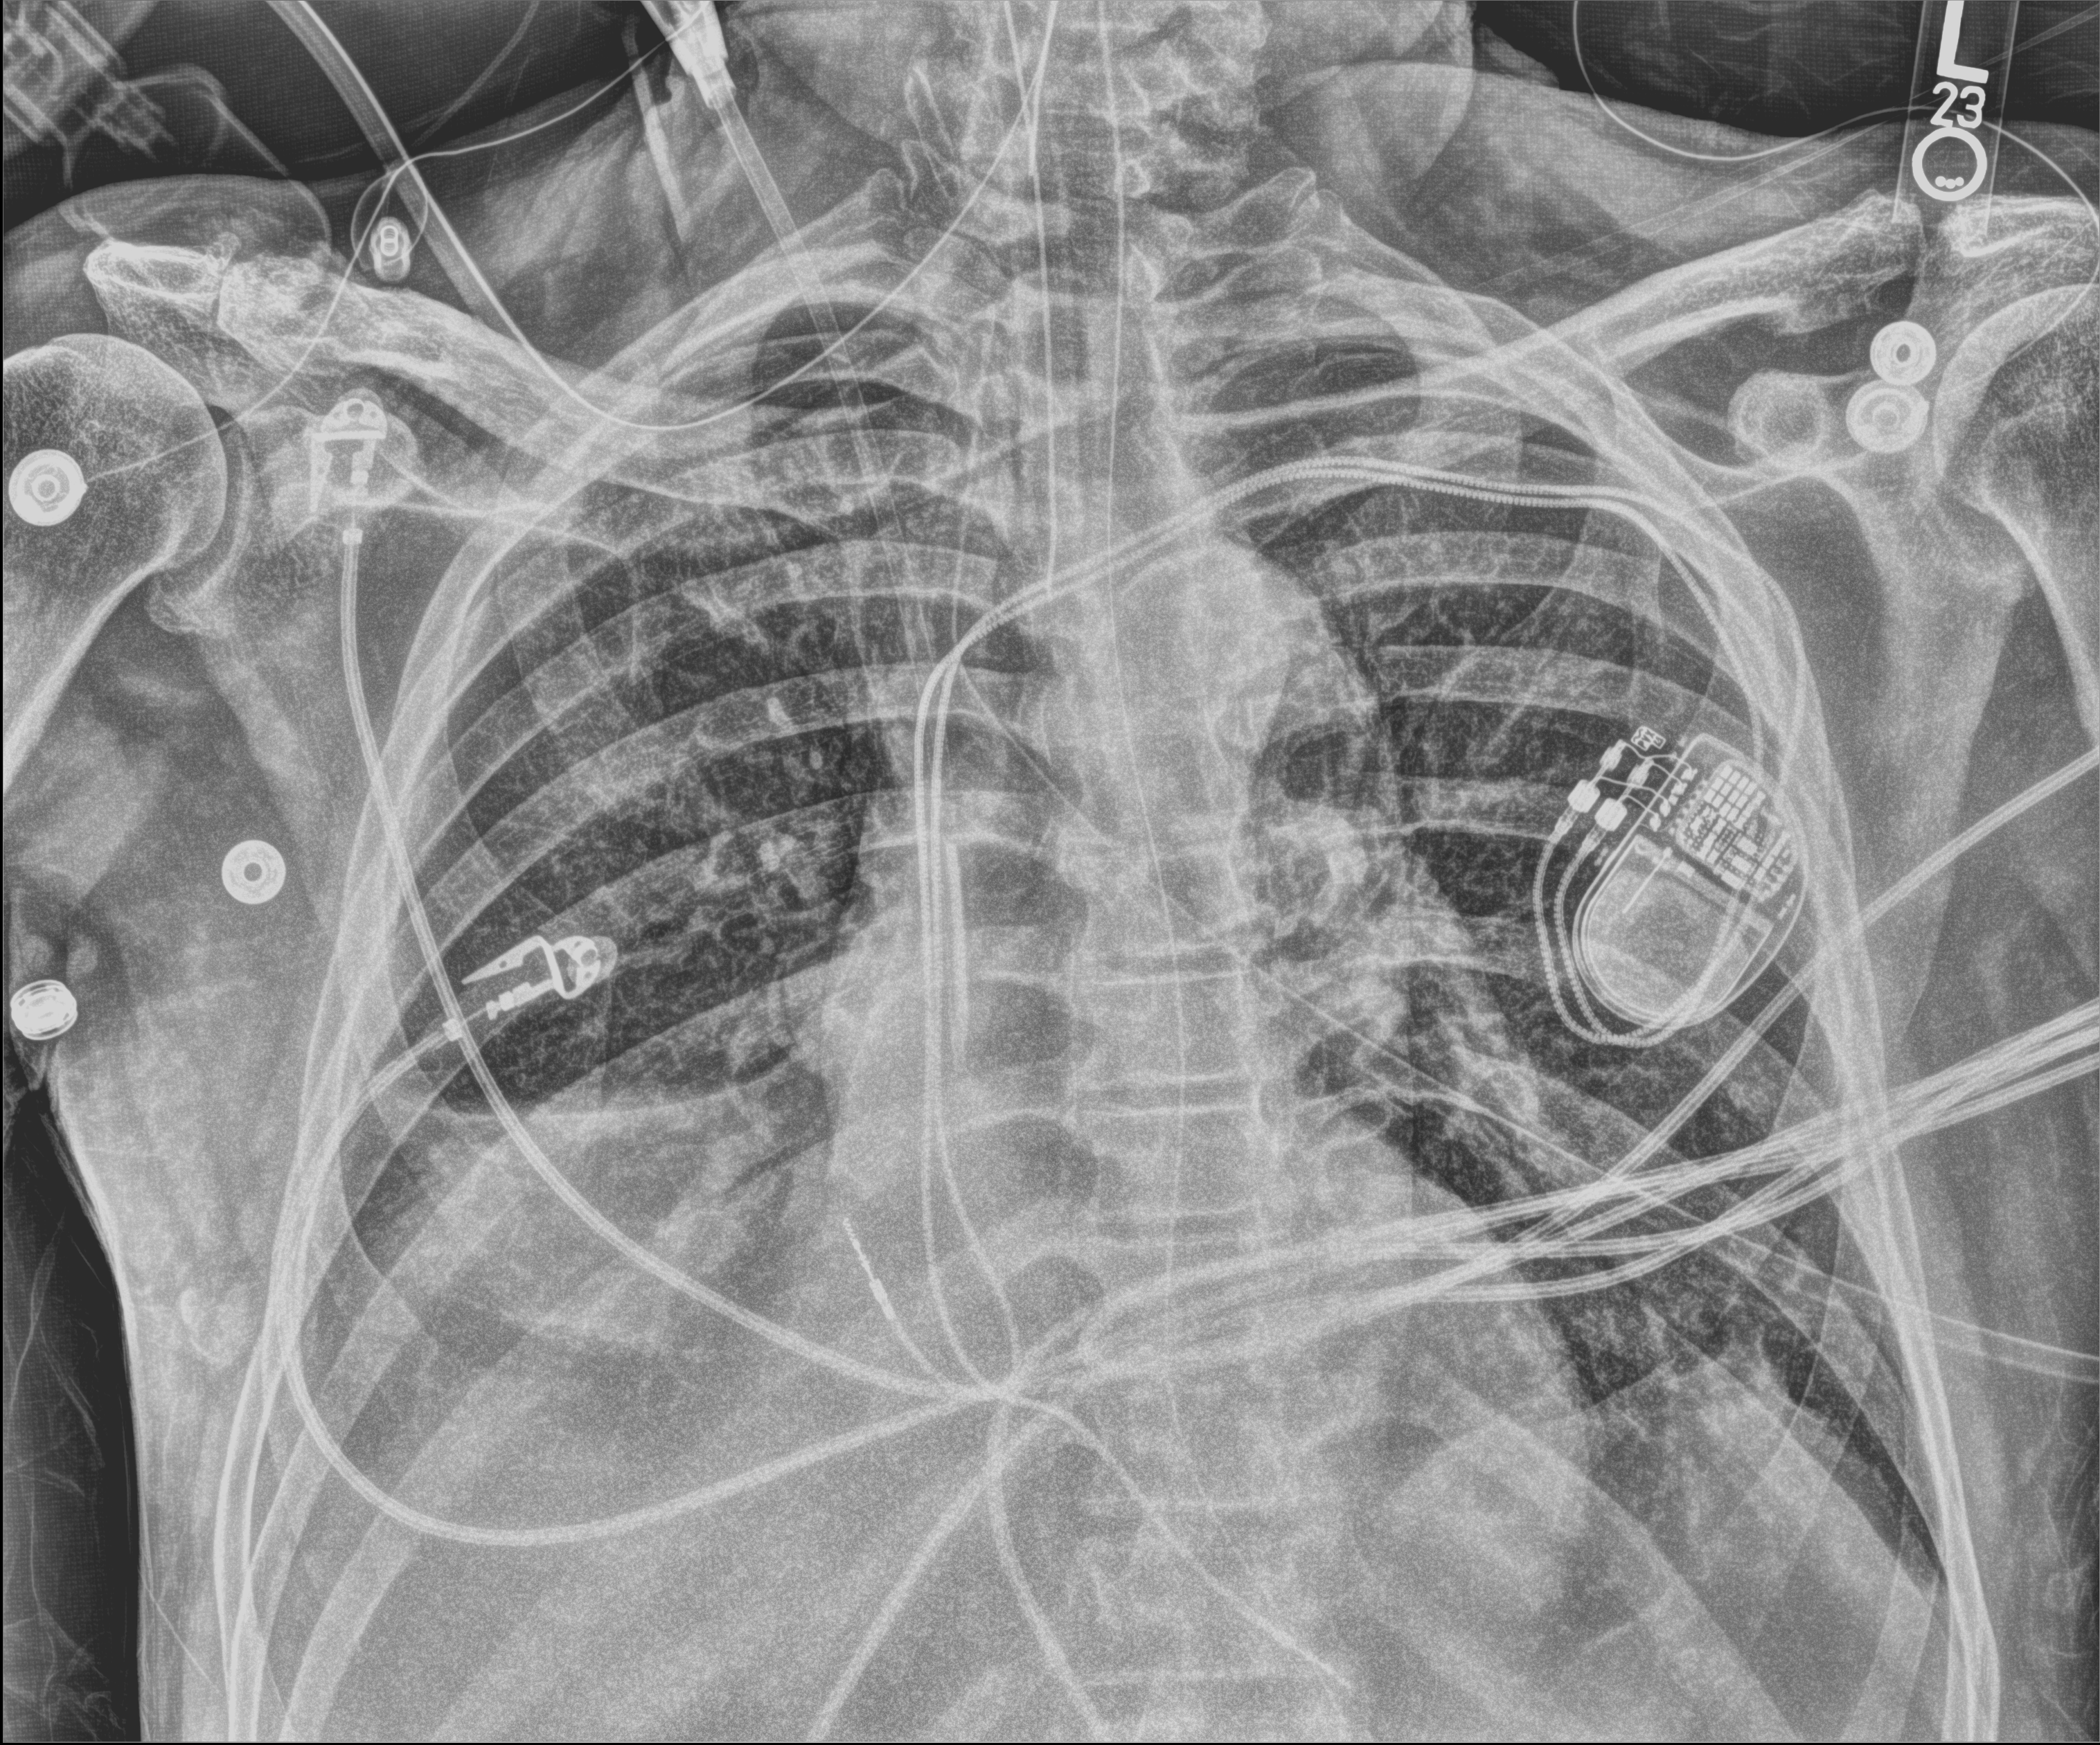
Chest X-ray (portable); anteroposterior (AP) projection. Male patient hospitalised with COVID-19, age 60–74 years.
Hospital-stay facts (about this admission, not read from this image; timing relative to this image not recorded): mechanically ventilated during this hospital stay: yes; admitted to intensive care during this hospital stay: yes.